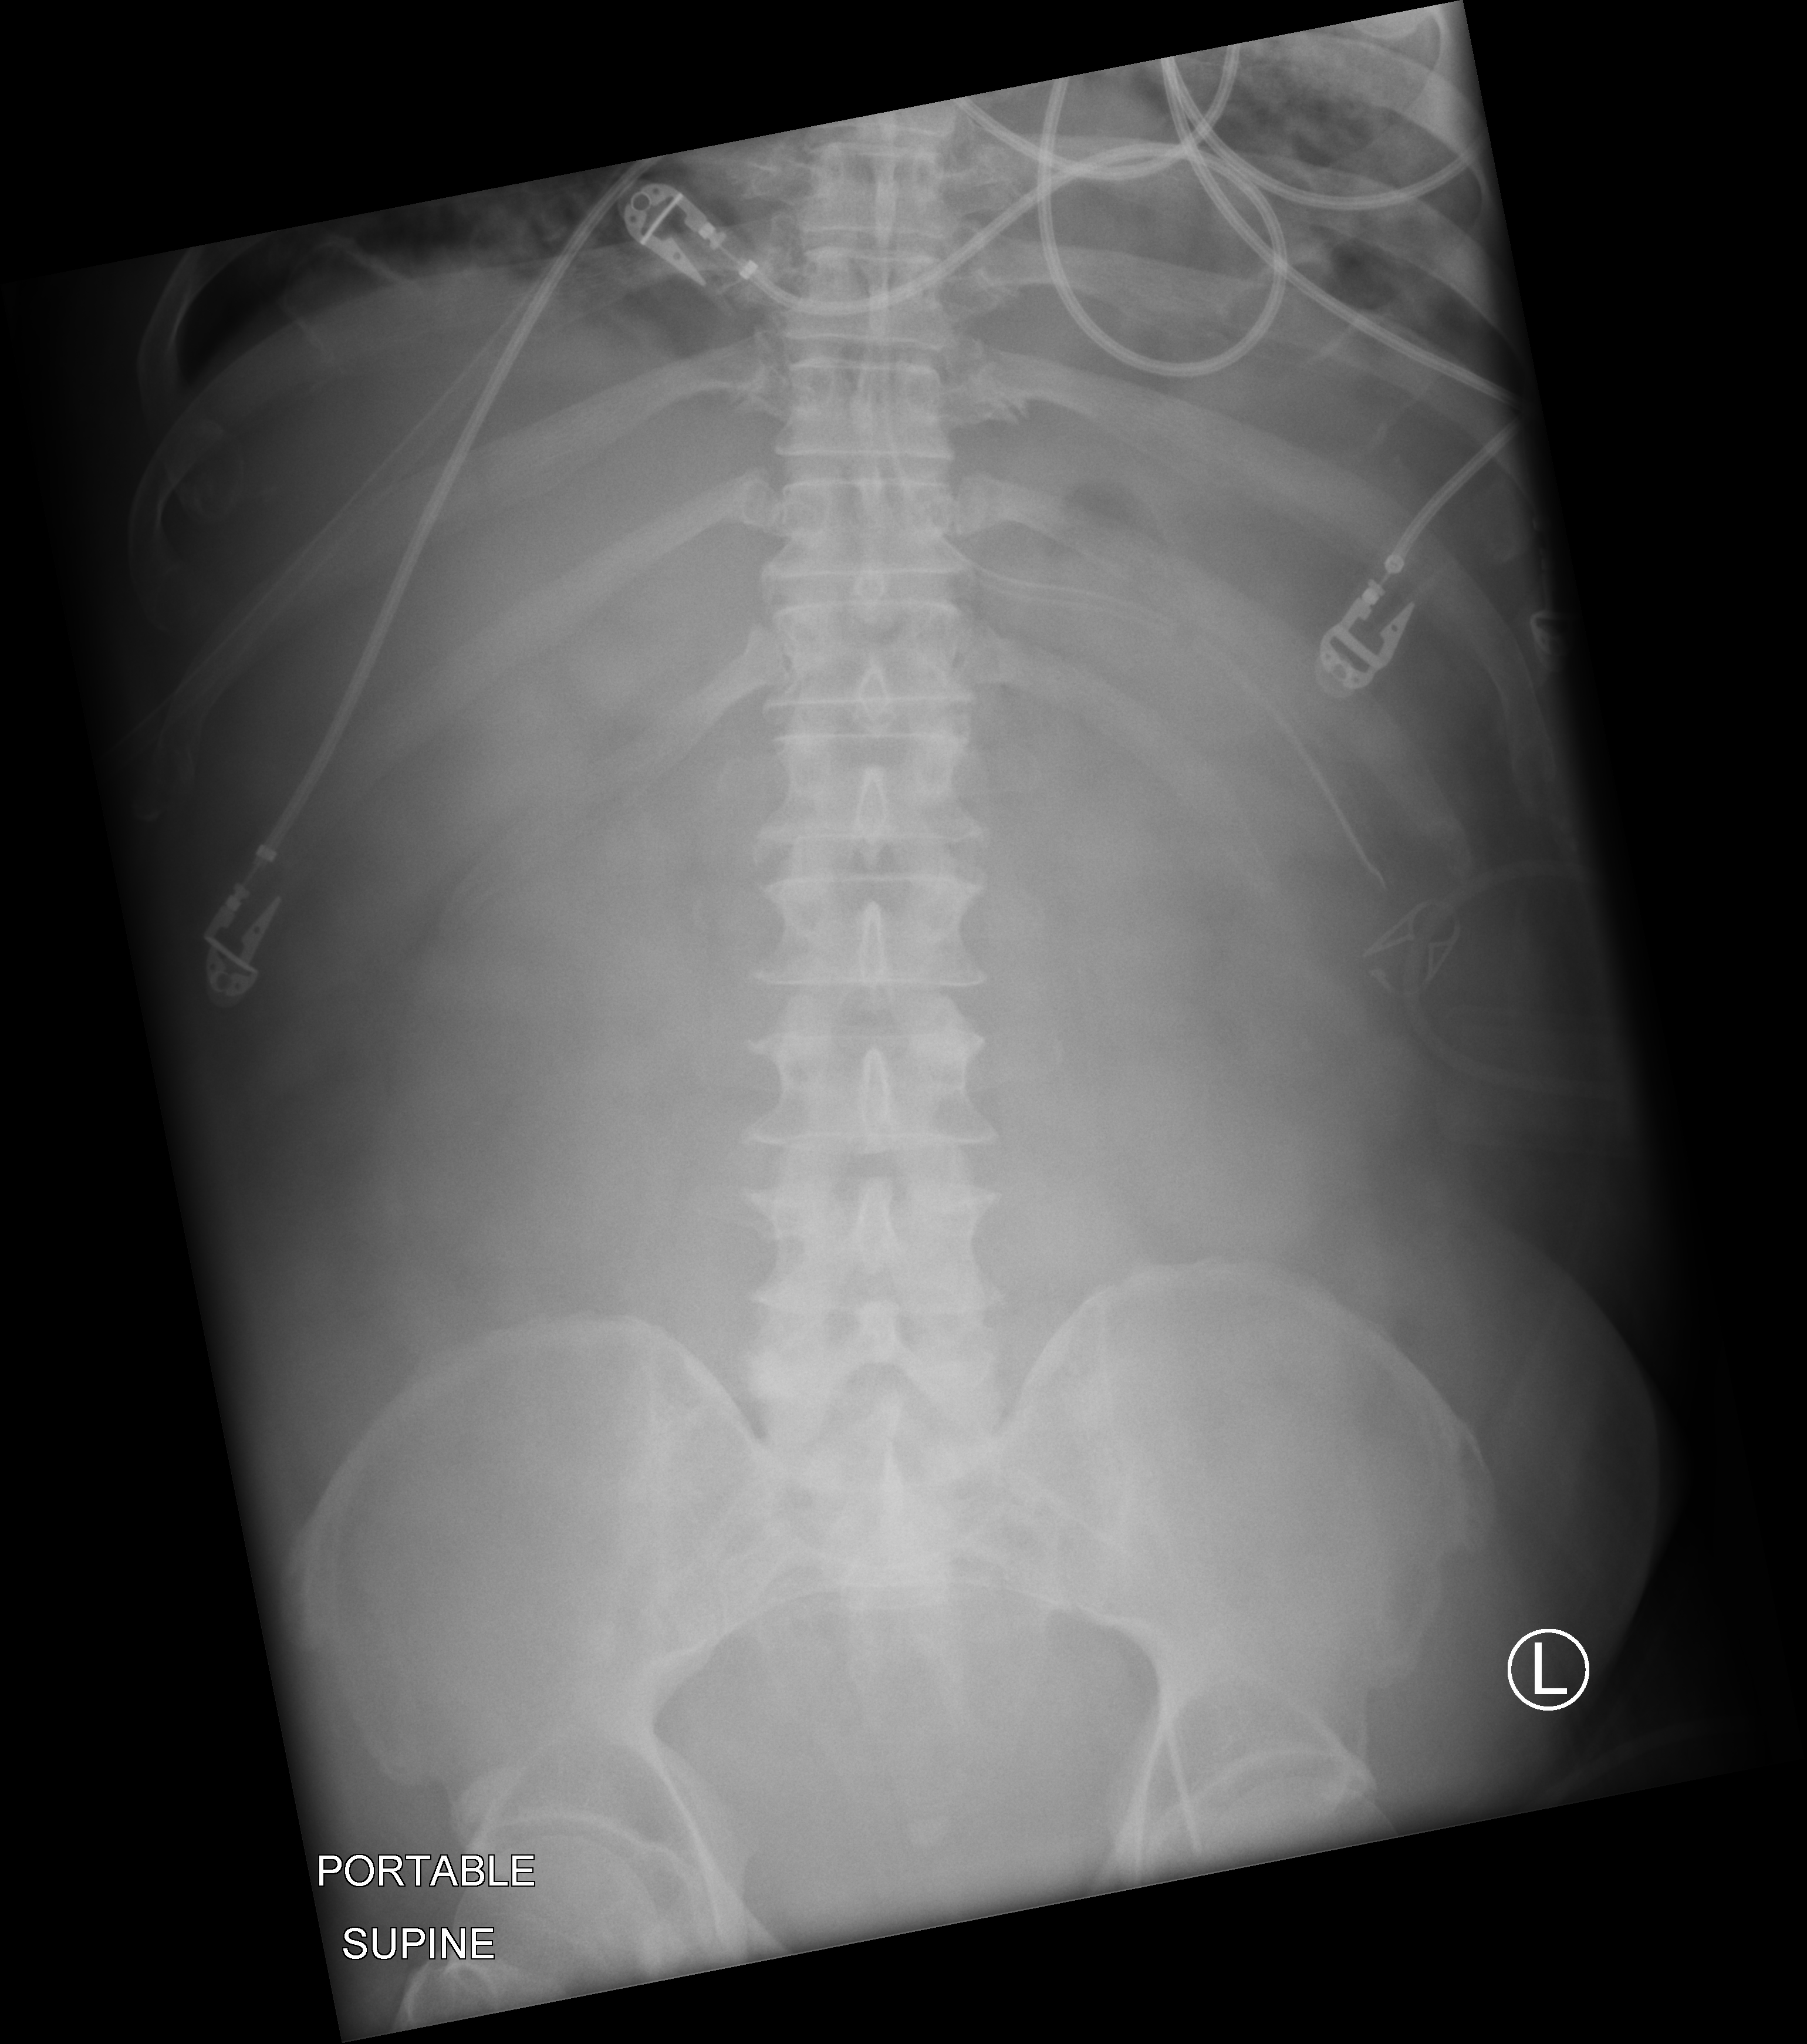
Portable abdomen radiograph, anteroposterior (AP) projection. Male patient hospitalised with COVID-19, age 60–74 years.
Hospital-stay facts (about this admission, not read from this image; timing relative to this image not recorded):
- admitted to intensive care during this hospital stay: yes